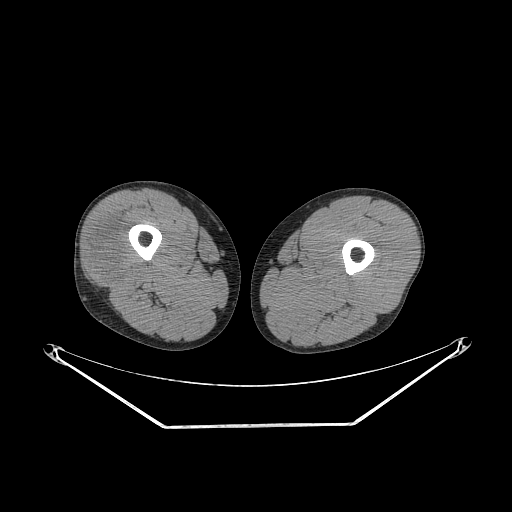
CT of an extremity soft-tissue mass (from a PET/CT study), one axial slice; position 229 of 267 along the scan axis; 140 kVp; soft-tissue window (W 400 / L 40 HU); 512 × 512 image matrix, field of view 500 × 500 mm. Male patient. Case-level facts recorded for this patient, not image findings: histological type: poorly differentiated synovial sarcoma; grade: high; site of the primary tumour: right buttock.
Structures marked on this image (expert contour drawn on MRI and transferred to this co-registered scan by the dataset authors):
- gross tumour volume including surrounding oedema: bounding box (x1, y1, x2, y2) in pixels: (91, 228, 138, 284)
- gross tumour volume (mass): (94, 233, 117, 277)